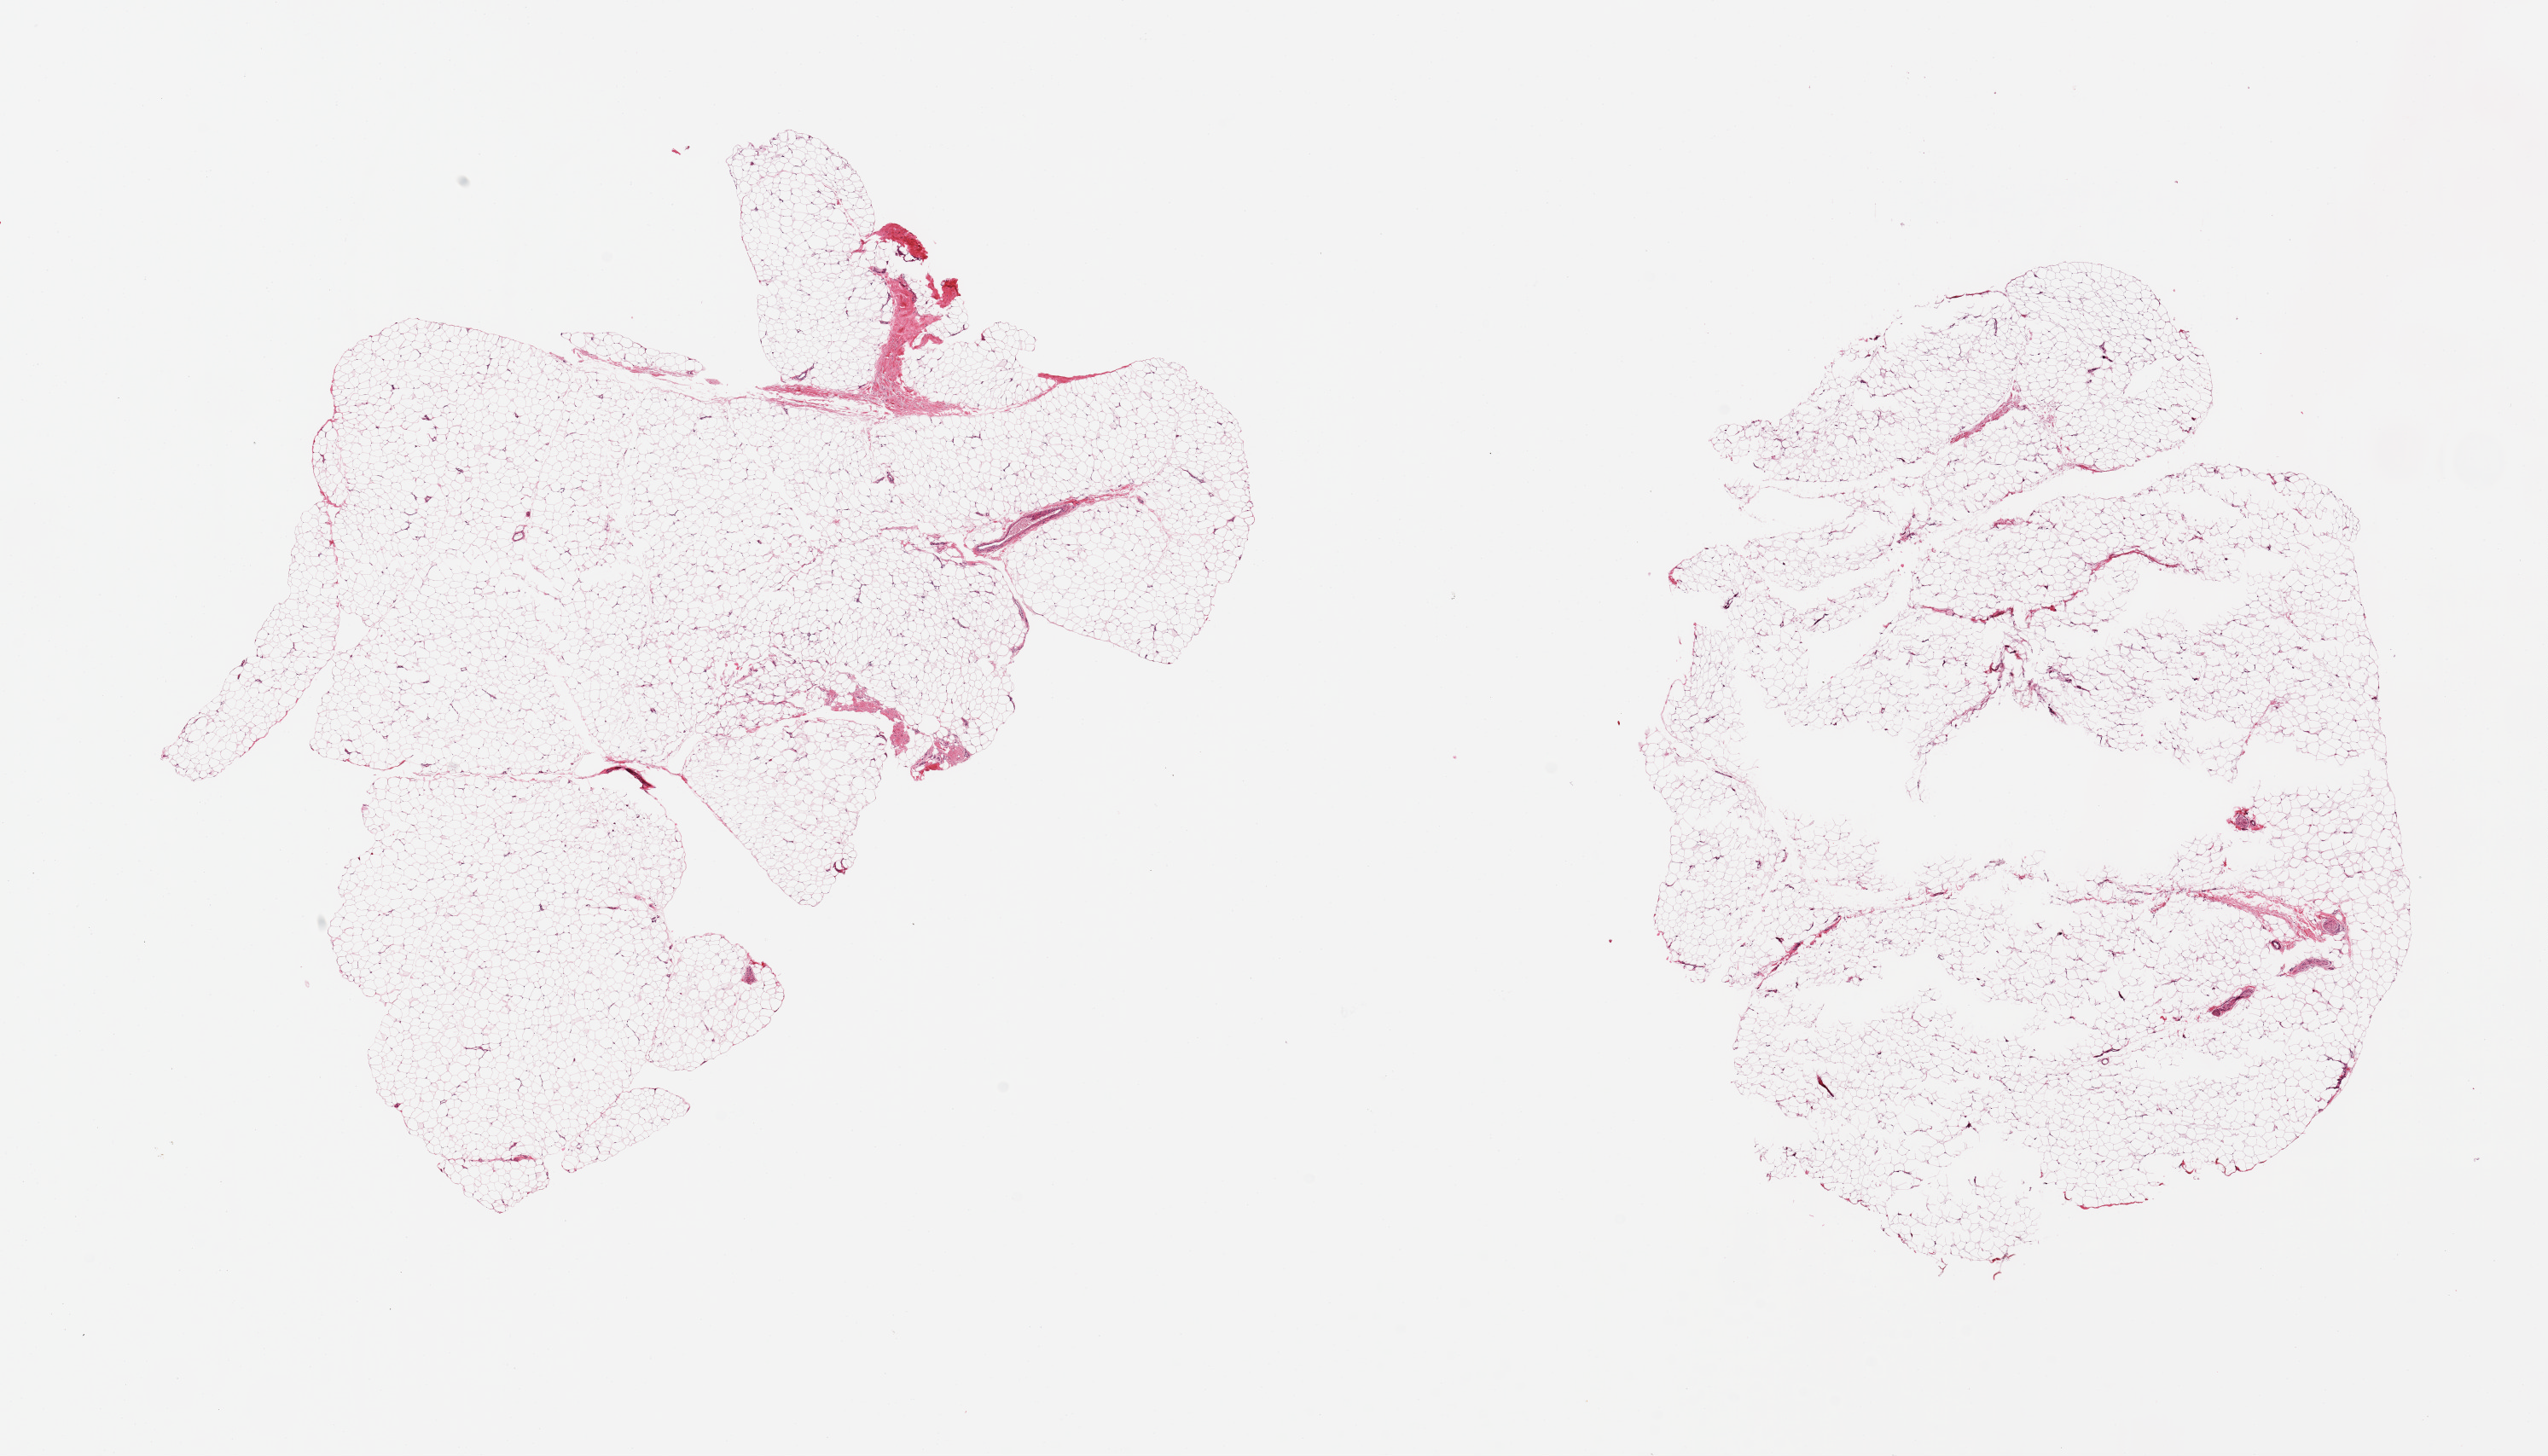
Digitized hematoxylin and eosin (H&E)-stained section, a low-resolution overview of the entire scanned area, about 23.6 x 13.5 mm (from a 20x scan); PAXgene-fixed paraffin-embedded (PFPE) section; sampled site (target tissue): adipose tissue; tissue donor sample. Donor: male.
Review note (as recorded): 2 pieces; mature adipose tissue with scant fibrovascular component and nerves.